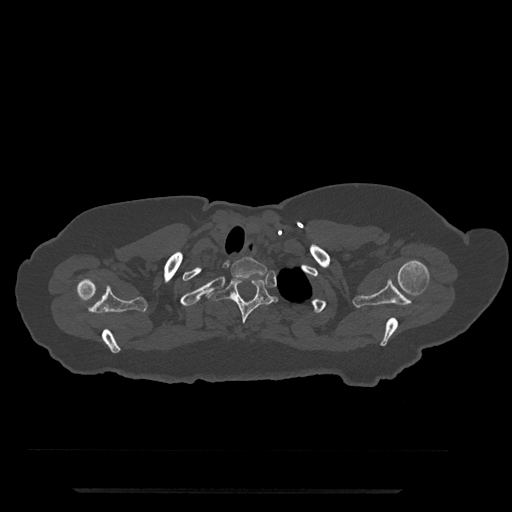
CT including the spine, one axial slice; position 682 of 797 along the scan axis; 120 kVp; bone window (W 1800 / L 400 HU); 0.5 mm slice thickness; 512 × 512 image matrix, field of view 440 × 440 mm. Patient: female, 51 years. Case-level facts recorded for this patient, not image findings: primary cancer: neuro; vertebrae with lytic lesions (as recorded): T8.
Outlined on this slice (semi-automatic segmentation, software-assisted and operator-edited):
- T1 vertebra: bounding box (x1, y1, x2, y2) in pixels: (231, 257, 267, 278)
- T2 vertebra: (207, 277, 278, 324)